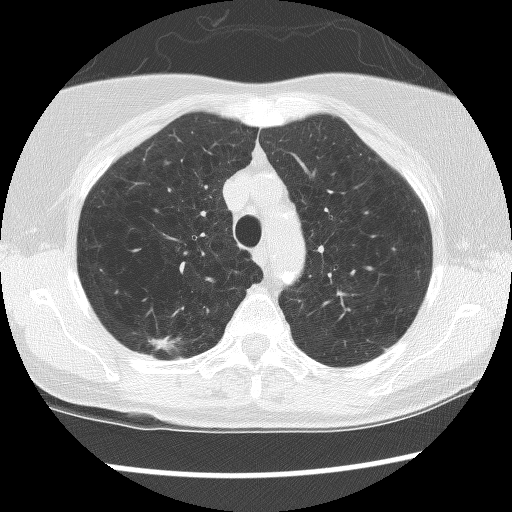
Axial slice from a low-dose chest CT screening exam; second screening round (one year after baseline); lung window (W 1500 / L -600 HU); 2.5 mm slice thickness; slice 31 of 134 in the series; 512 × 512 image matrix, field of view 320 × 320 mm. Female participant, aged 63 years at enrolment. Former smoker at enrolment.
Expert reader's lesion annotation, bounding box [x1, y1, x2, y2] px = [133, 318, 197, 369]. The exam's reader record, not a measurement of the box and not confirmed to be the same lesion: non-calcified nodule or mass ≥4 mm, right upper lobe, 16 × 7 mm, spiculated (stellate) margins, mixed attenuation, pre-existing on the prior screen: yes; interval growth: yes.